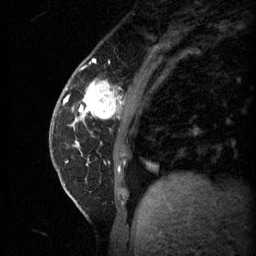
Breast MRI (dynamic contrast-enhanced), one sagittal slice. Position 14 of 60 along the scan axis. 3 images stored at this slice position (order not interpretable as contrast timing). 1.5 T. TE 4.2 ms, TR 11 ms. 2 mm slice thickness. 256 × 256 image matrix, field of view 180 × 180 mm. Female patient, age 62 years.
Outlined on this slice (semi-automatic segmentation, software-assisted and operator-edited):
- analysis volume of interest (the breast-tissue region the enhancement analysis was run in; not a lesion): bounding box [x1, y1, x2, y2] px = [55, 72, 124, 131]
- tumour enhancement mask (voxels above the 70 % enhancement threshold inside the analysis volume of interest): [66, 82, 117, 121]